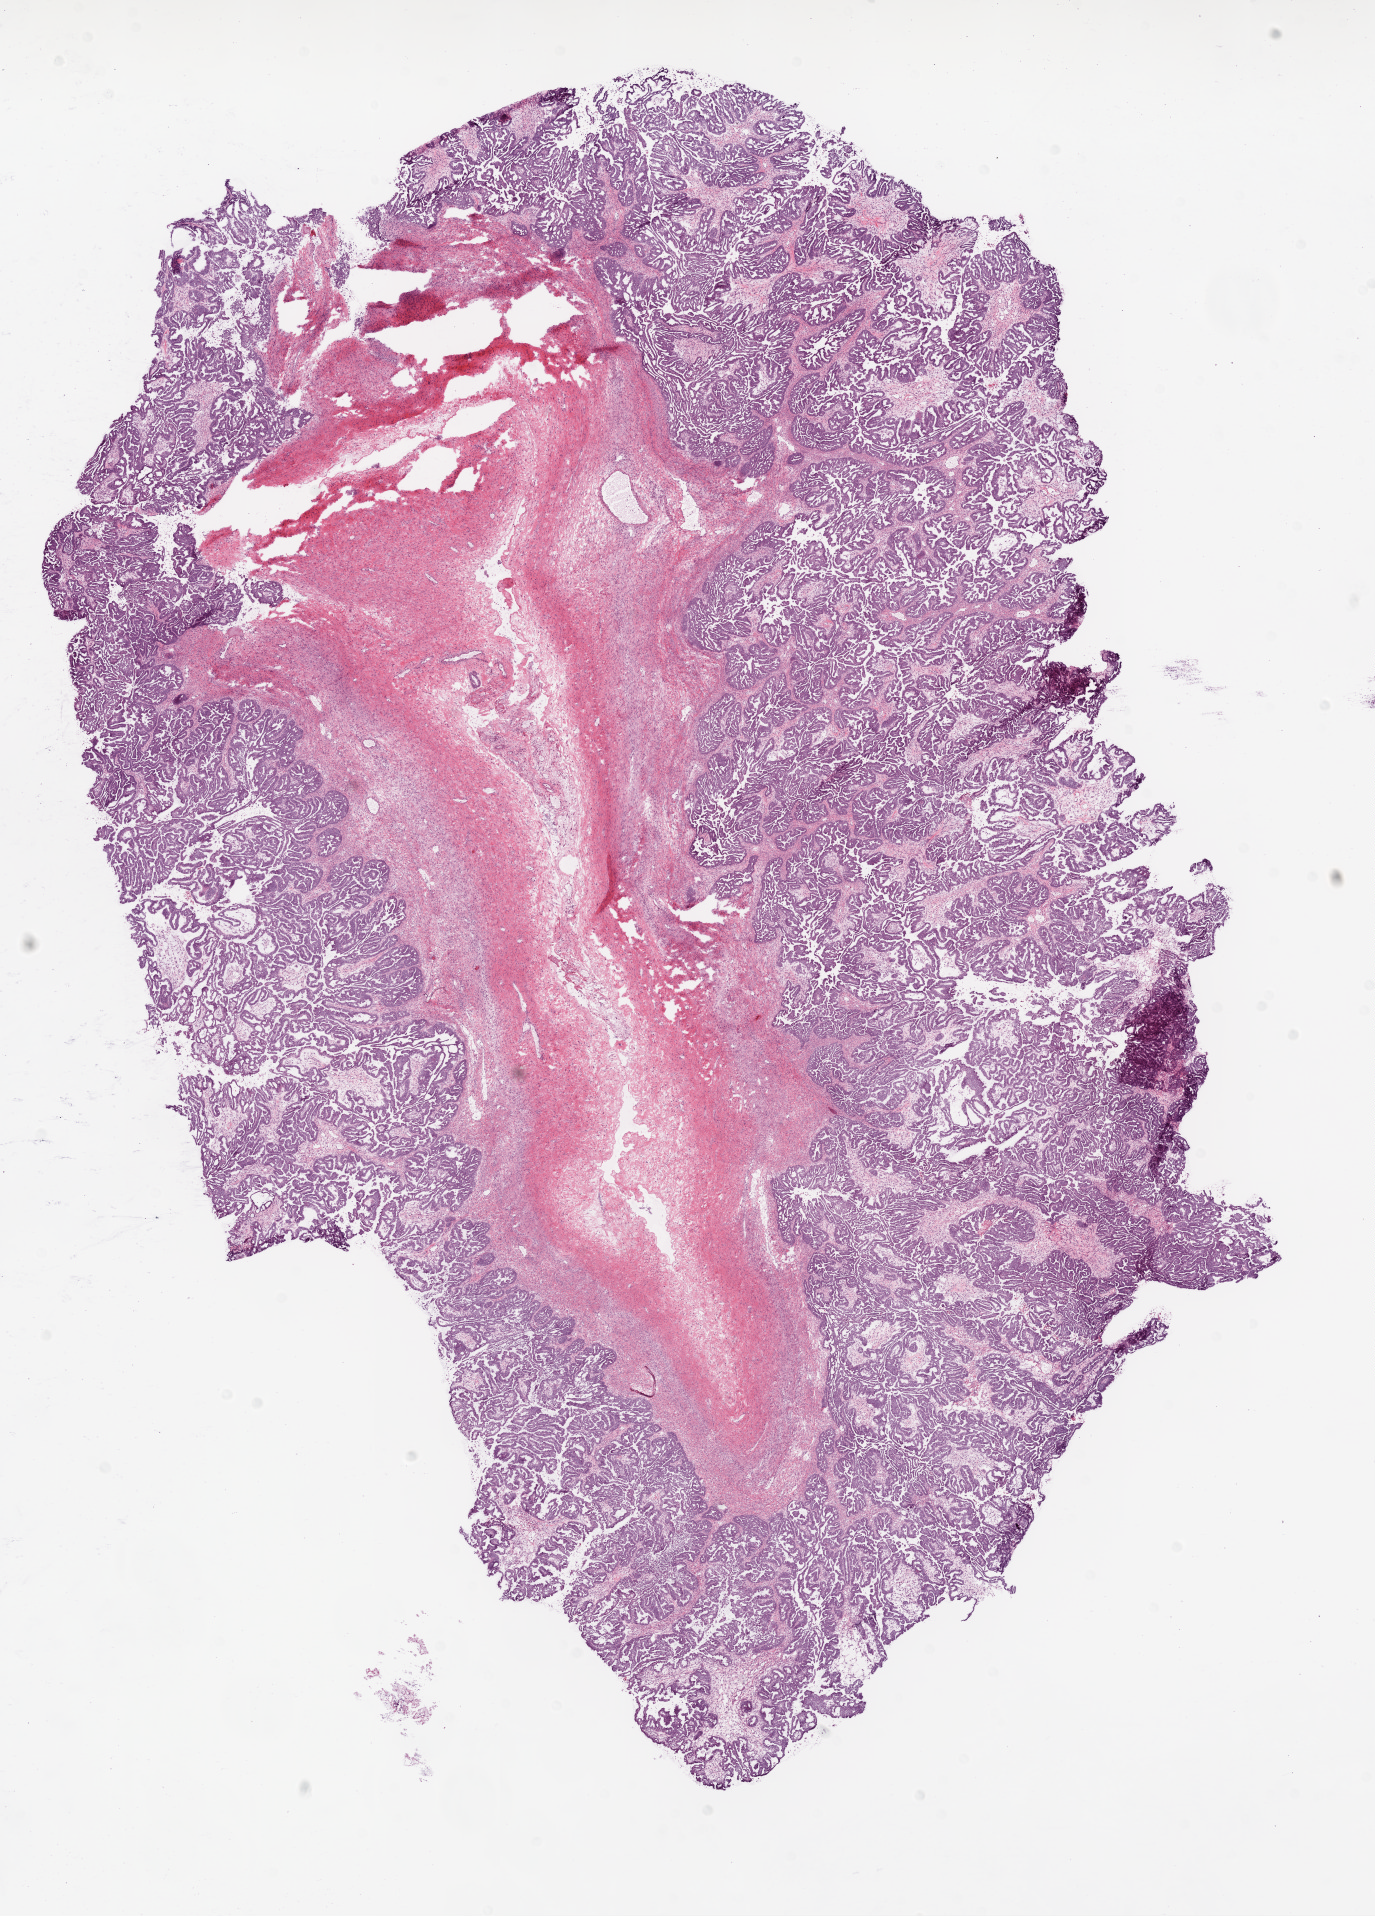
Whole-slide histology image, Hematoxylin and eosin (H&E) stained, whole scanned area (about 11.0 x 15.4 mm) shown as a low-resolution overview; frozen section from the bottom of the tissue portion; primary tumour sample from the ovary. Female, age 37 years at initial diagnosis. Histologic grade: G1 (well differentiated). Composition of this section per pathologist review: tumour cells 75%, tumour nuclei 90%, normal cells 18%, stromal cells 5%, necrosis 2%.
Laterality: bilateral. Histologic diagnosis: Serous cystadenocarcinoma, NOS. FIGO stage: IIIC.